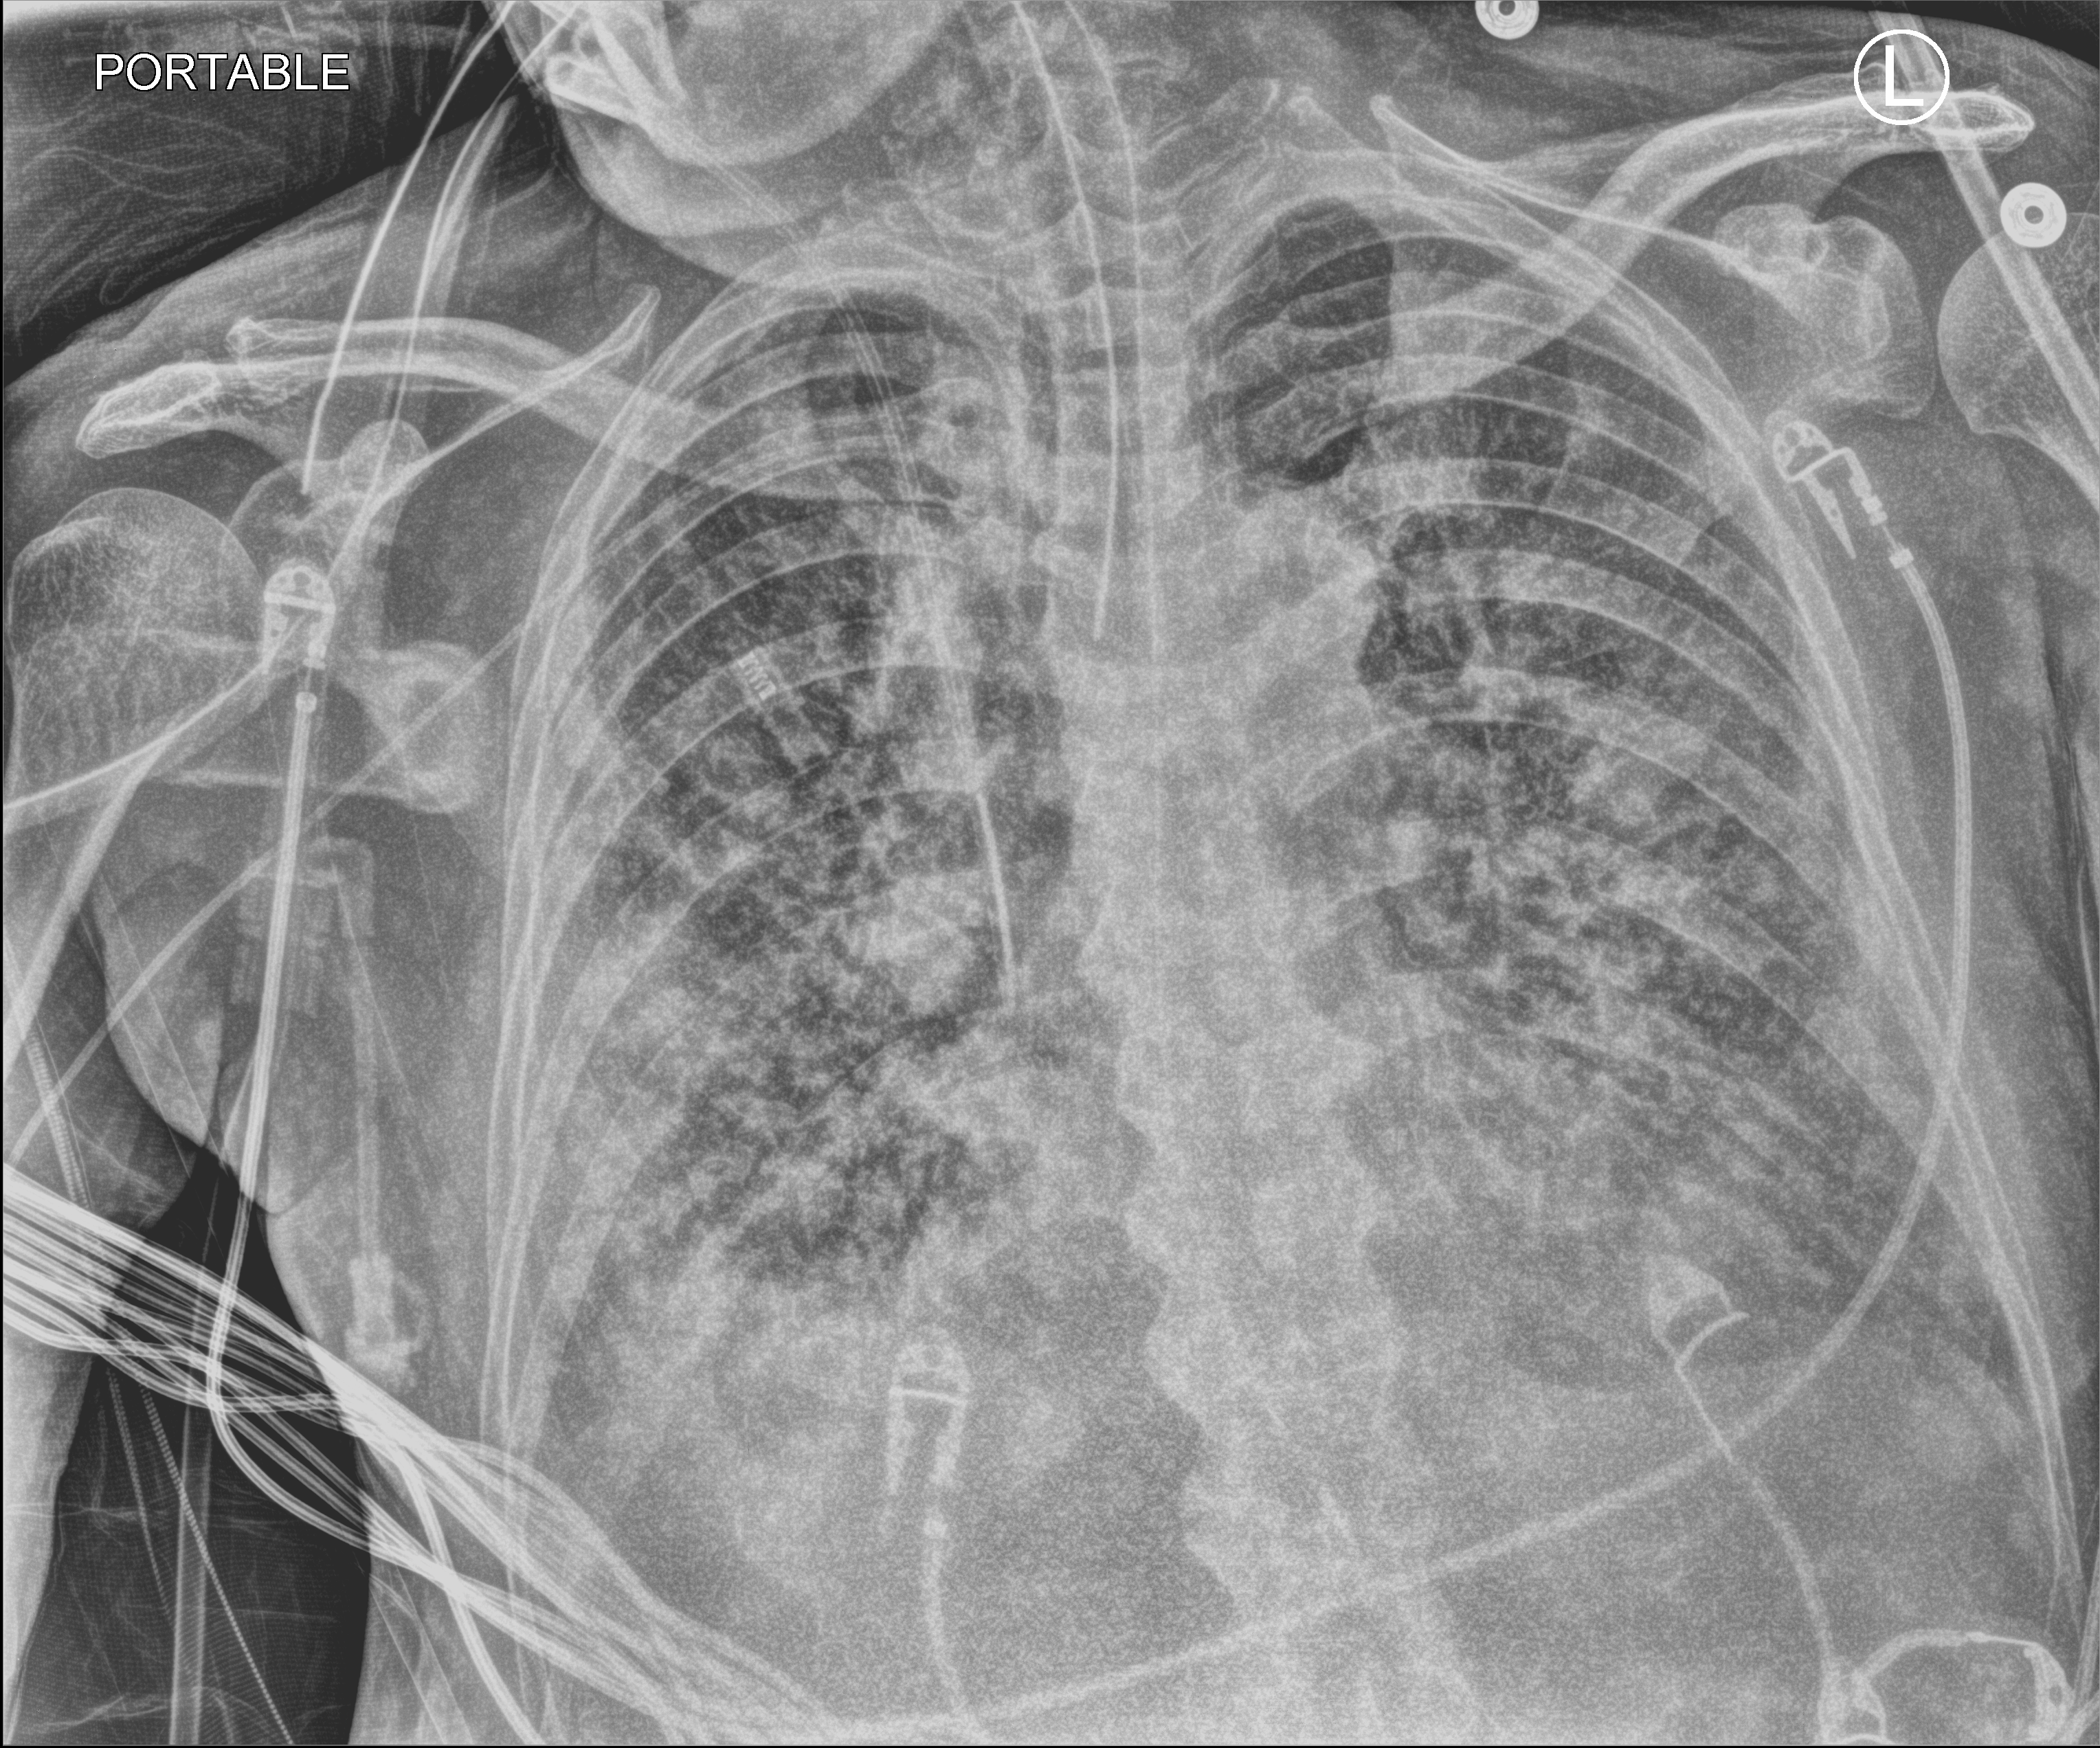
Portable chest radiograph; anteroposterior (AP) projection. Male patient hospitalised with COVID-19, age 60–74 years.
Hospital-stay facts (about this admission, not read from this image; timing relative to this image not recorded): other chronic lung disease (admission record): no; smoking status (admission record): never.